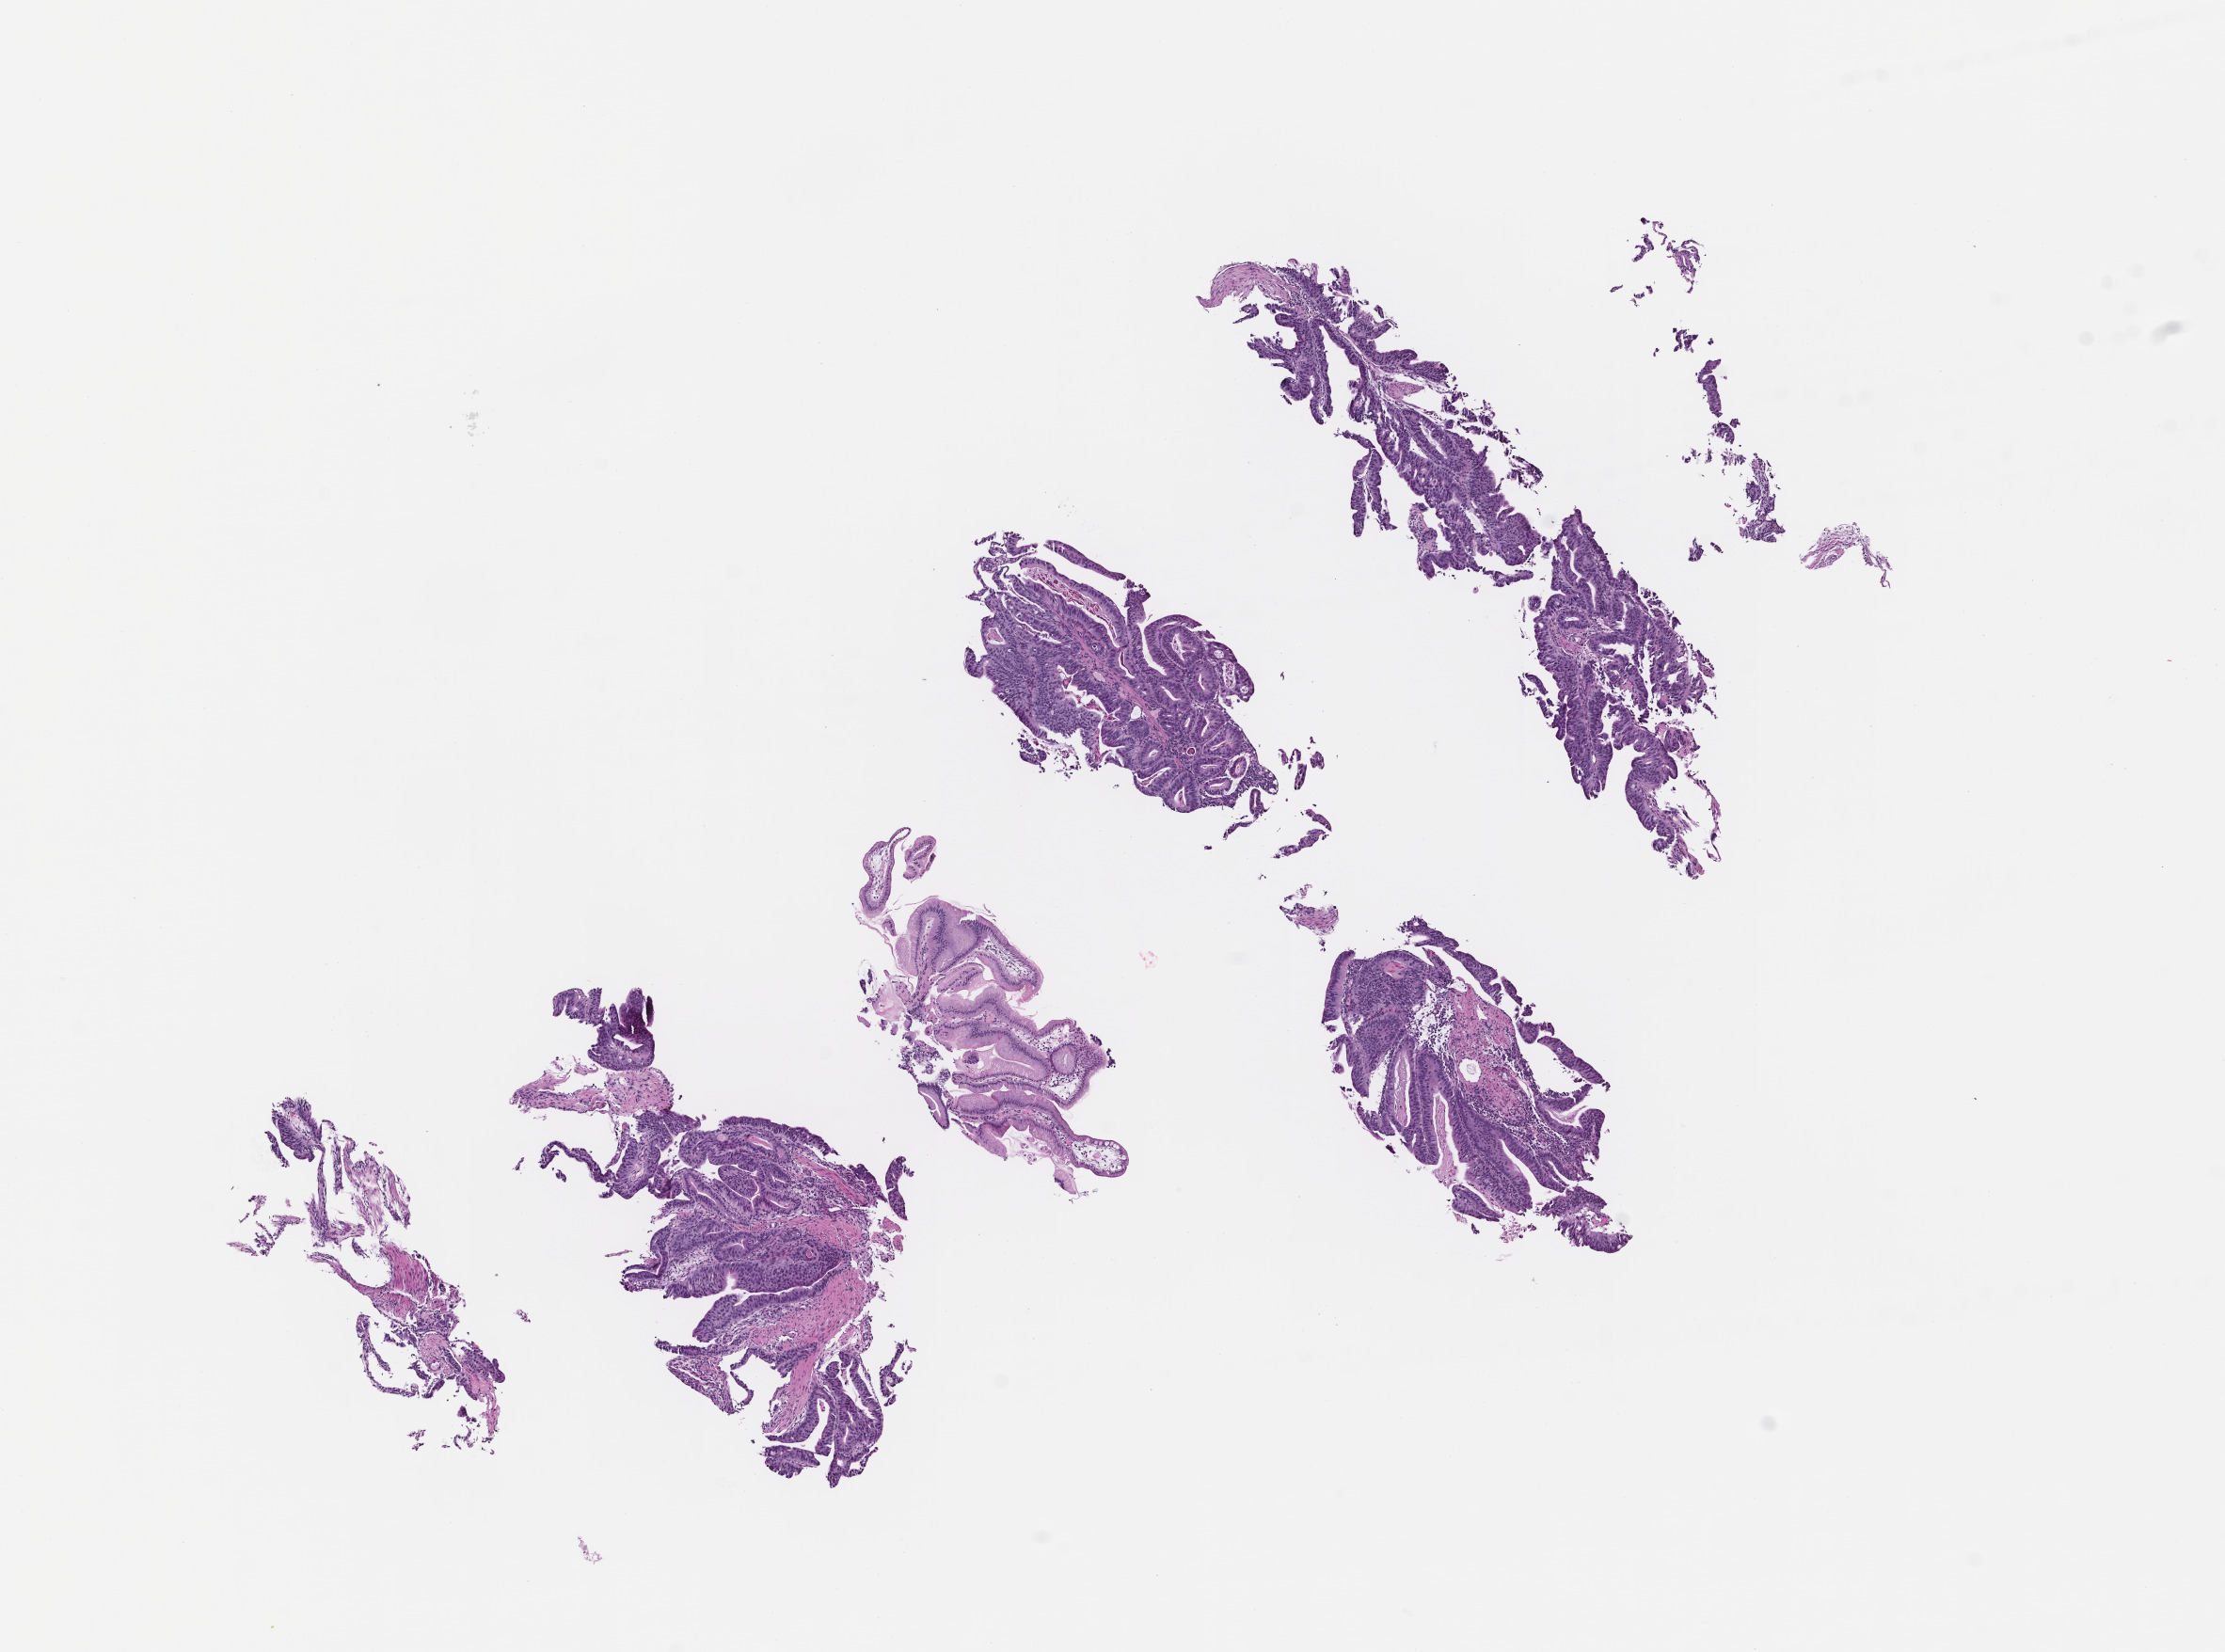
Whole-slide image, hematoxylin and eosin (H&E) stain, shown as a low-resolution overview of the whole scanned area (about 9.5 x 7.1 mm), FFPE section, specimen time point: archival tissue. Female patient.
* this section: metastasis (sampled organ not recorded)
* primary diagnosis of the patient: Gastric Carcinoma